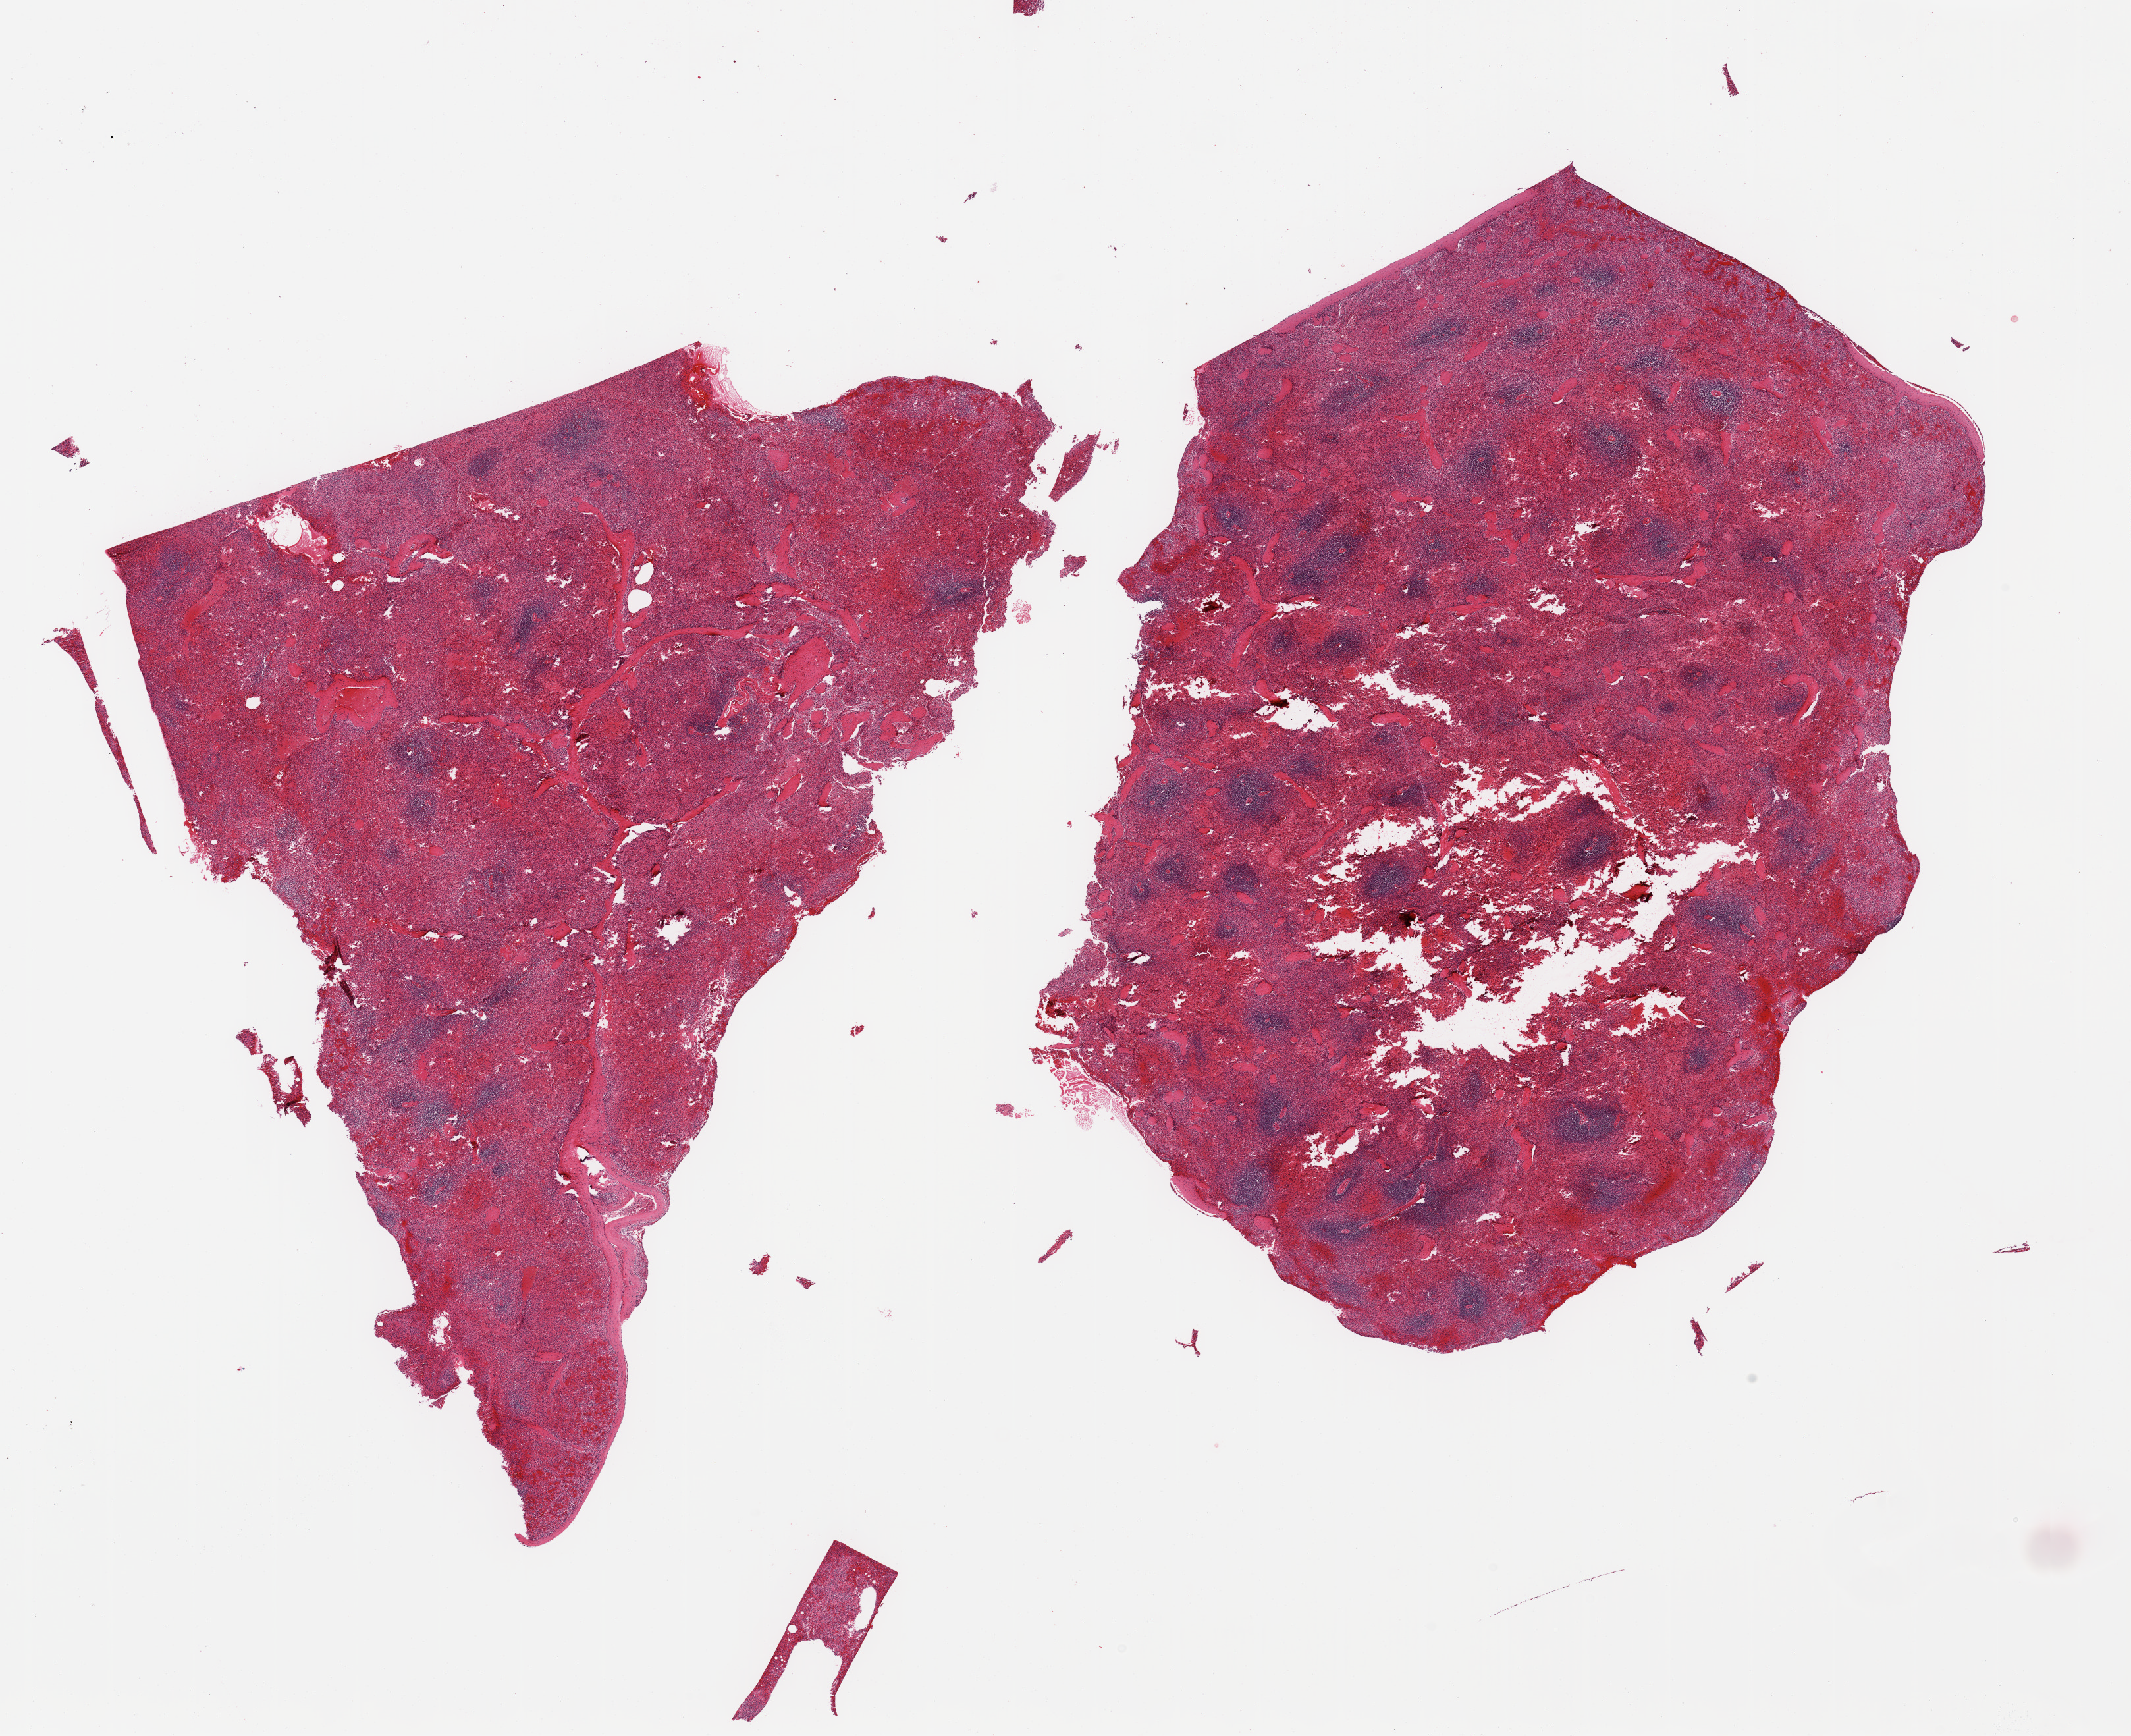
Digitized haematoxylin and eosin-stained section — low-resolution overview of the scanned area, about 25.6 x 20.8 mm; PAXgene-fixed, paraffin-embedded tissue; section of spleen (target tissue); tissue donor sample.
Reviewer comment on this tissue sample: 2 pieces; includes portion of capsule (target is 5mm below capsule), some congestion.